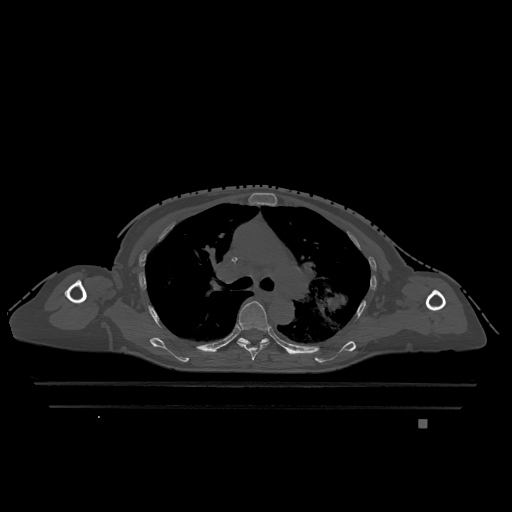
CT including the spine, one axial slice. Slice 820 of 1317 in the series (ordered by position). Bone window (W 1800 / L 400 HU). 512 × 512 image matrix, field of view 500 × 500 mm. Female patient, age 74 years. From the clinical record (not read from this slice): primary cancer: lung; vertebrae with lytic lesions (as recorded): T1, T4, T5, T6, L4, L5.
Outlined on this slice (semi-automatically segmented with operator editing):
- T5 vertebra: bounding box (x1, y1, x2, y2) in pixels: (238, 301, 269, 361)
- T6 vertebra: (238, 337, 269, 344)